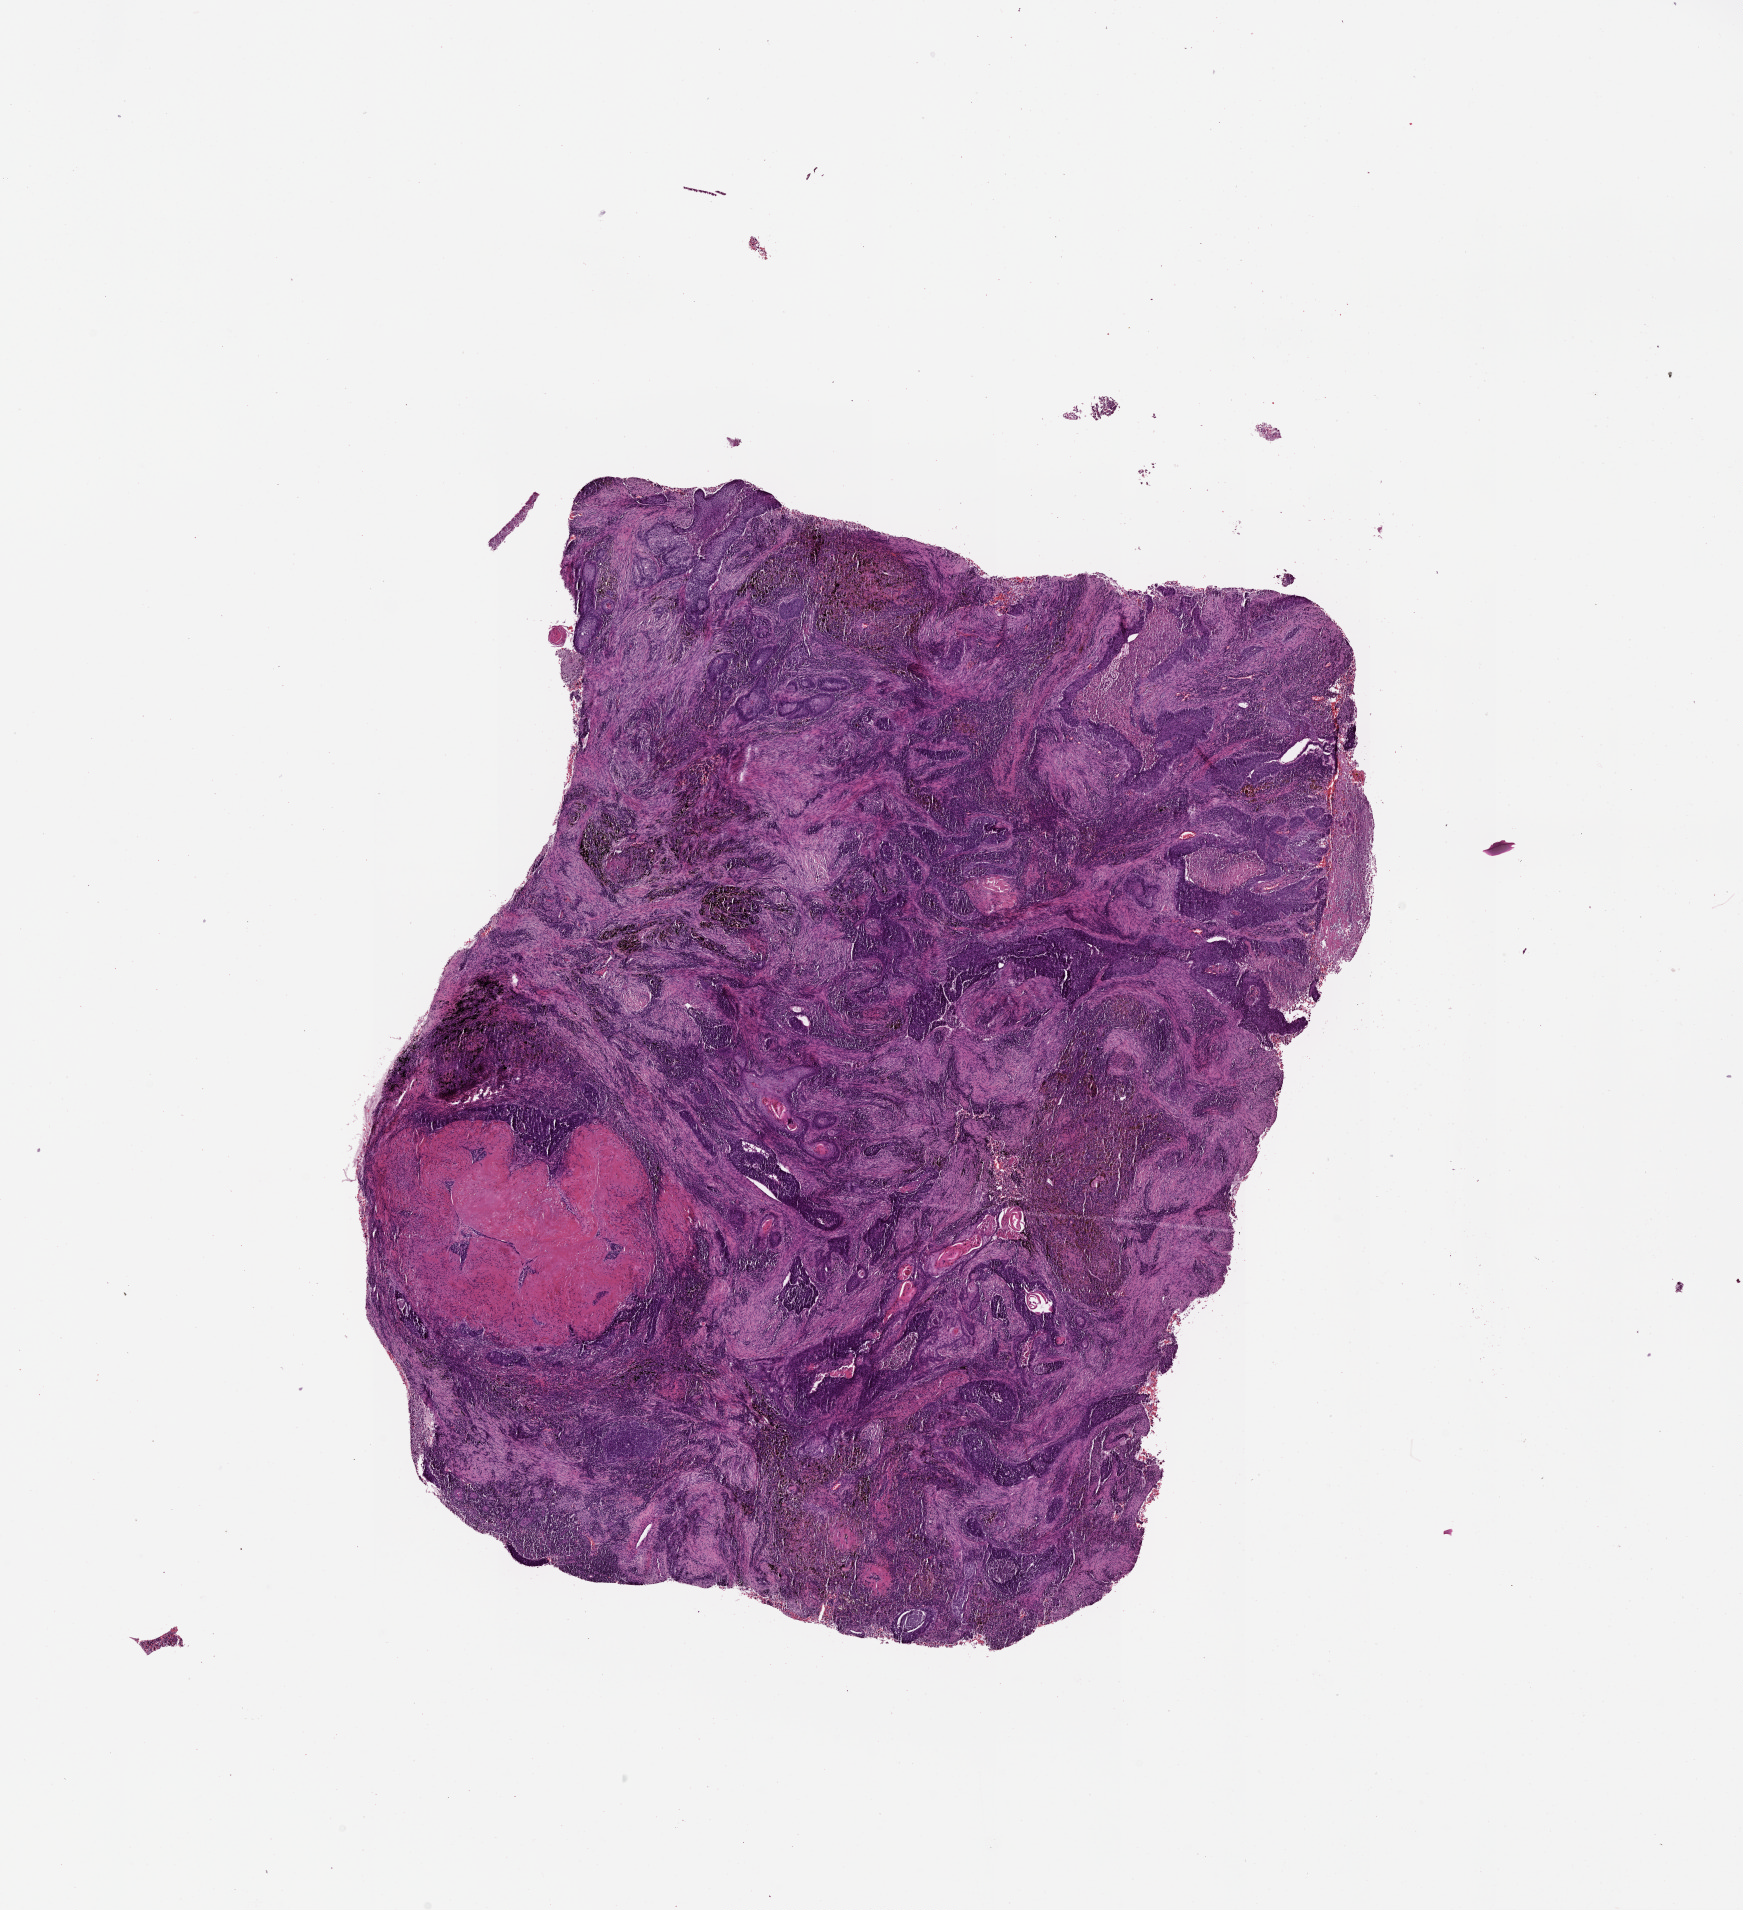
Whole-slide histology image, H&E, shown as a low-resolution overview of the whole scanned area (about 14.0 x 15.4 mm), lung, tumour tissue. 59-year-old male patient.
Patient diagnosis (cohort enrolment): squamous cell carcinoma (lung).